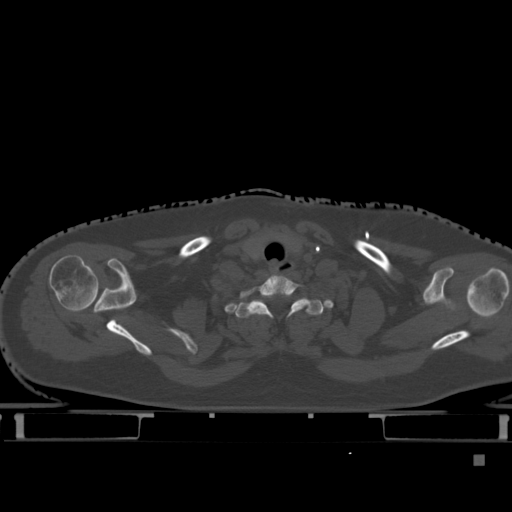
CT including the spine, one axial slice; position 376 of 495 along the scan axis; bone window (W 1800 / L 400 HU); 1.5 mm slice thickness; 512 × 512 image matrix, field of view 404 × 404 mm. Female patient, age 33 years. Case-level facts recorded for this patient, not image findings: primary cancer: breast; vertebrae with lytic lesions (as recorded): T1.
Annotated regions visible in this slice (semi-automatically segmented with operator editing):
- T1 vertebra: box from (x=235, y=292) to (x=323, y=322) px